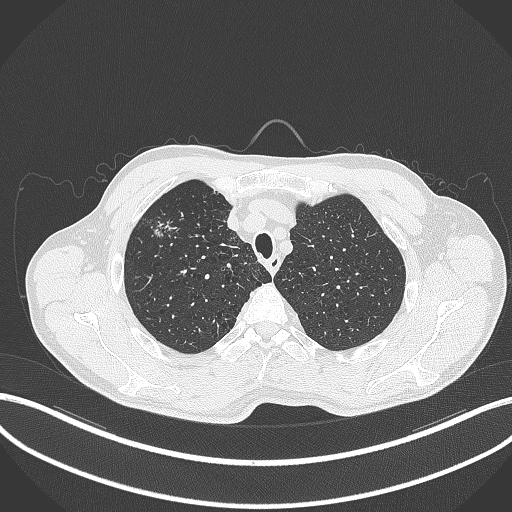
Chest CT, one axial slice; position 349 of 427 along the scan axis; 120 kVp; lung window (W 1500 / L -600 HU); 512 × 512 image matrix, field of view 400 × 400 mm. Patient: male, 69 years. From the clinical record (not read from this slice): clinical TNM (as recorded): T1b N1 M0.
Outlined on this slice (bounding box drawn by a radiologist):
- lung tumour (recorded histology: adenocarcinoma): box from (x=144, y=215) to (x=183, y=251) px